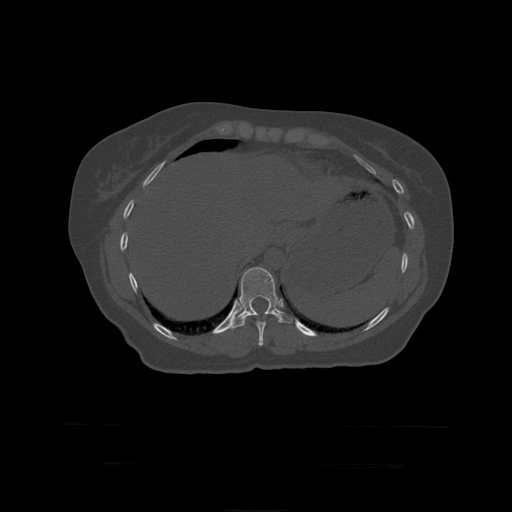
CT including the spine, one axial slice; position 228 of 399 along the scan axis; 120 kVp; bone window (W 1800 / L 400 HU); 1.25 mm slice thickness; 512 × 512 image matrix, field of view 450 × 450 mm. Patient age 41 years. From the clinical record (not read from this slice): primary cancer: breast.
Annotated regions visible in this slice (semi-automatically segmented with operator editing):
- T10 vertebra: box from (x=256, y=321) to (x=267, y=346) px
- T11 vertebra: (x=230, y=267)–(x=293, y=330)